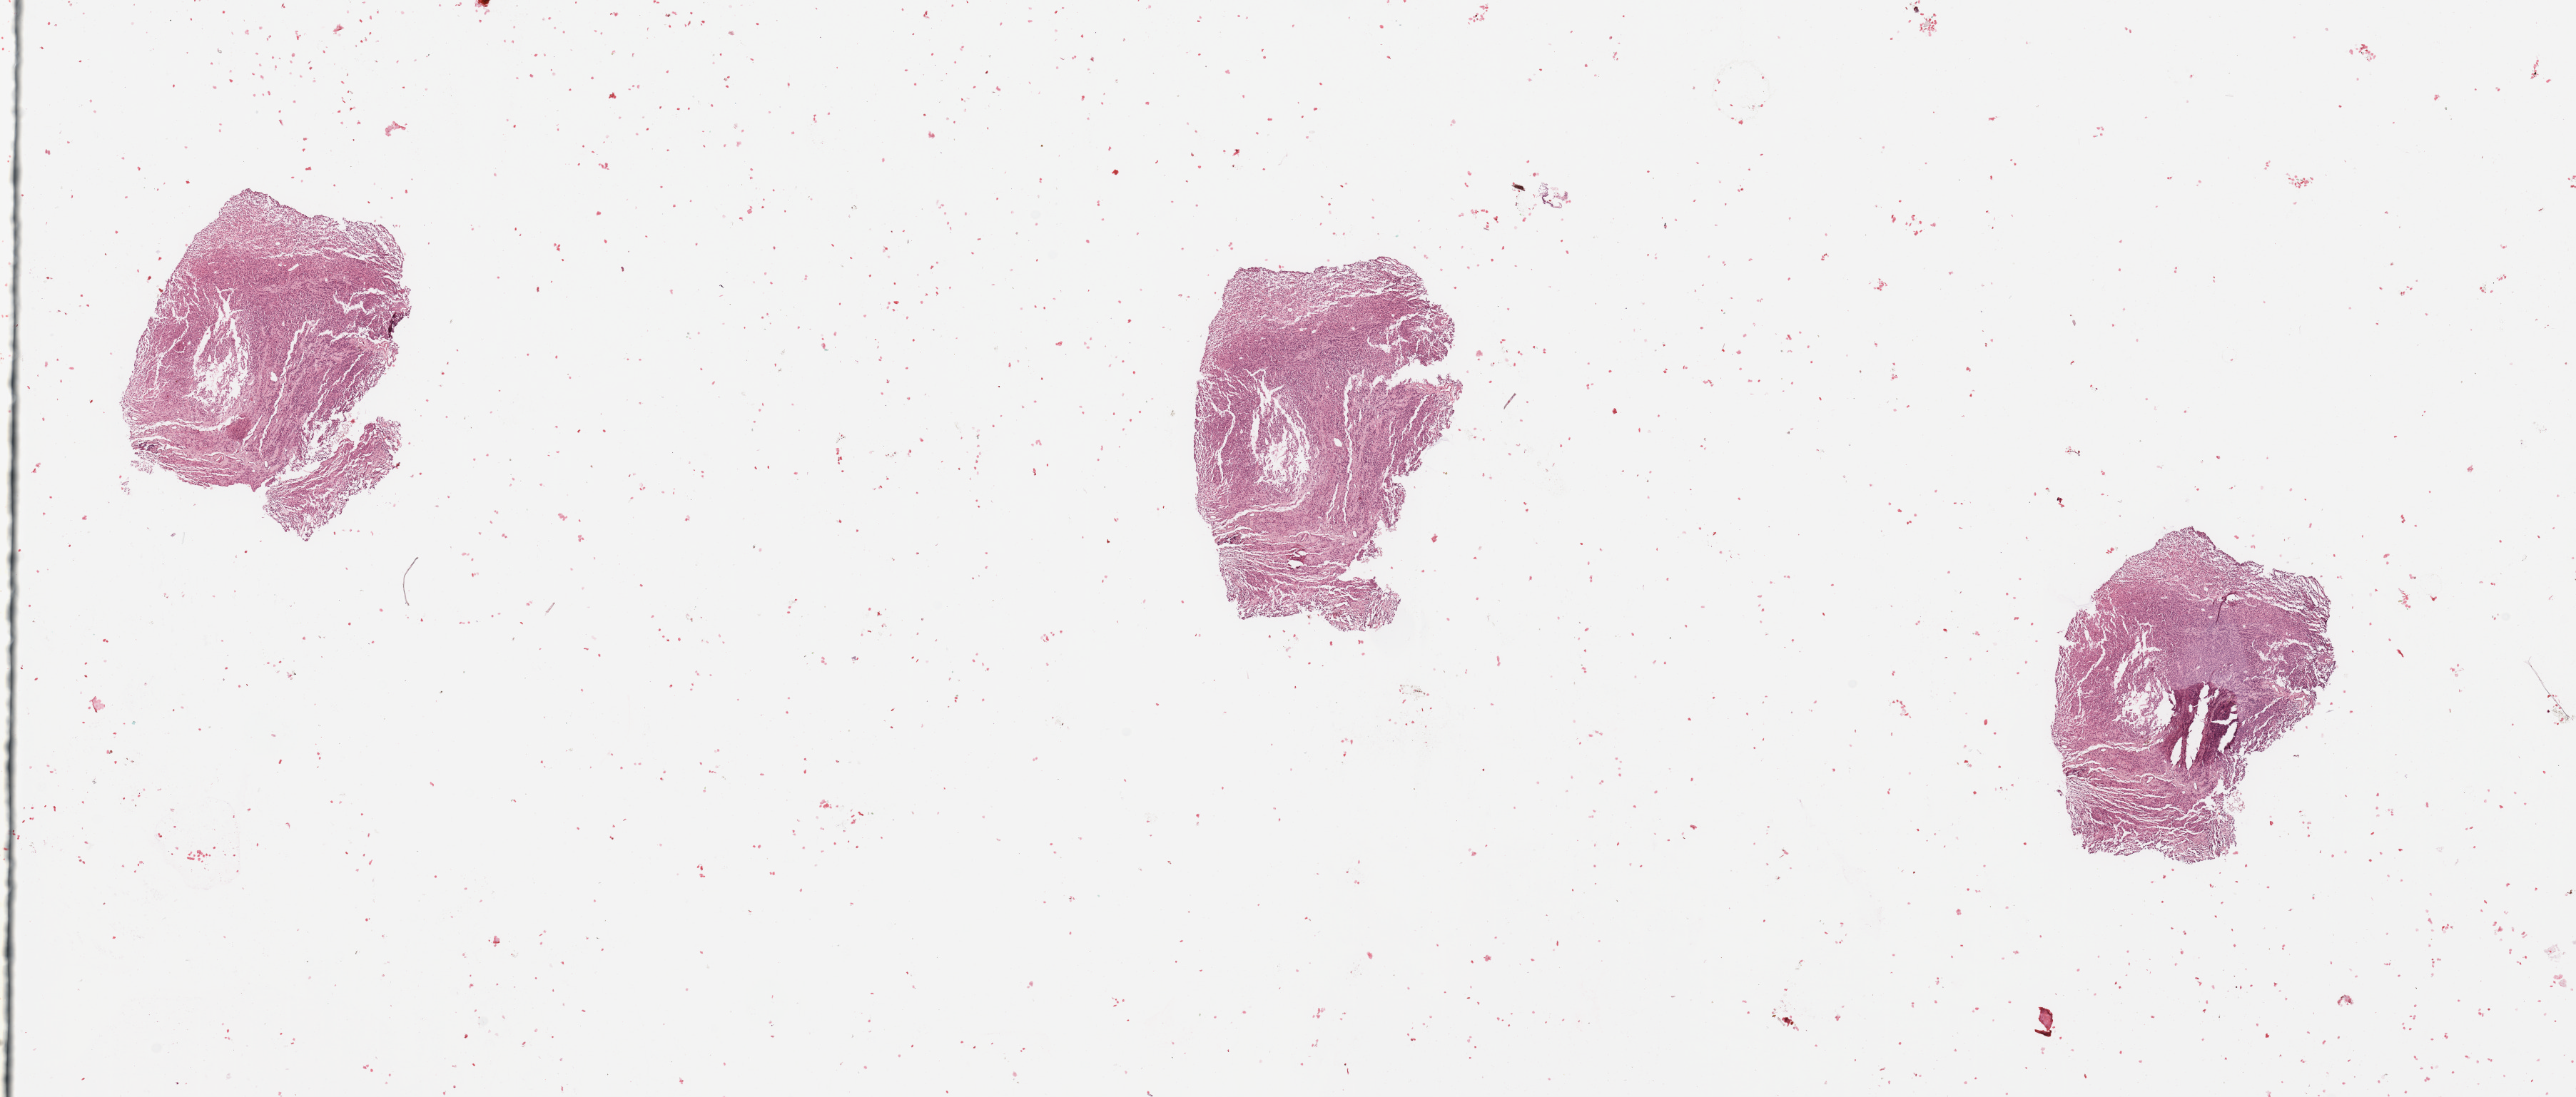
Digitized Hematoxylin and eosin (H&E) stained tissue section (whole slide), whole scanned area (about 28.5 x 12.2 mm) shown as a low-resolution overview; tumour tissue sample, sampled site: brain. Female, 34 y/o. Slide review estimates, as recorded: tumour nuclei 80%, necrosis 5%.
Diagnosis: Glioblastoma.